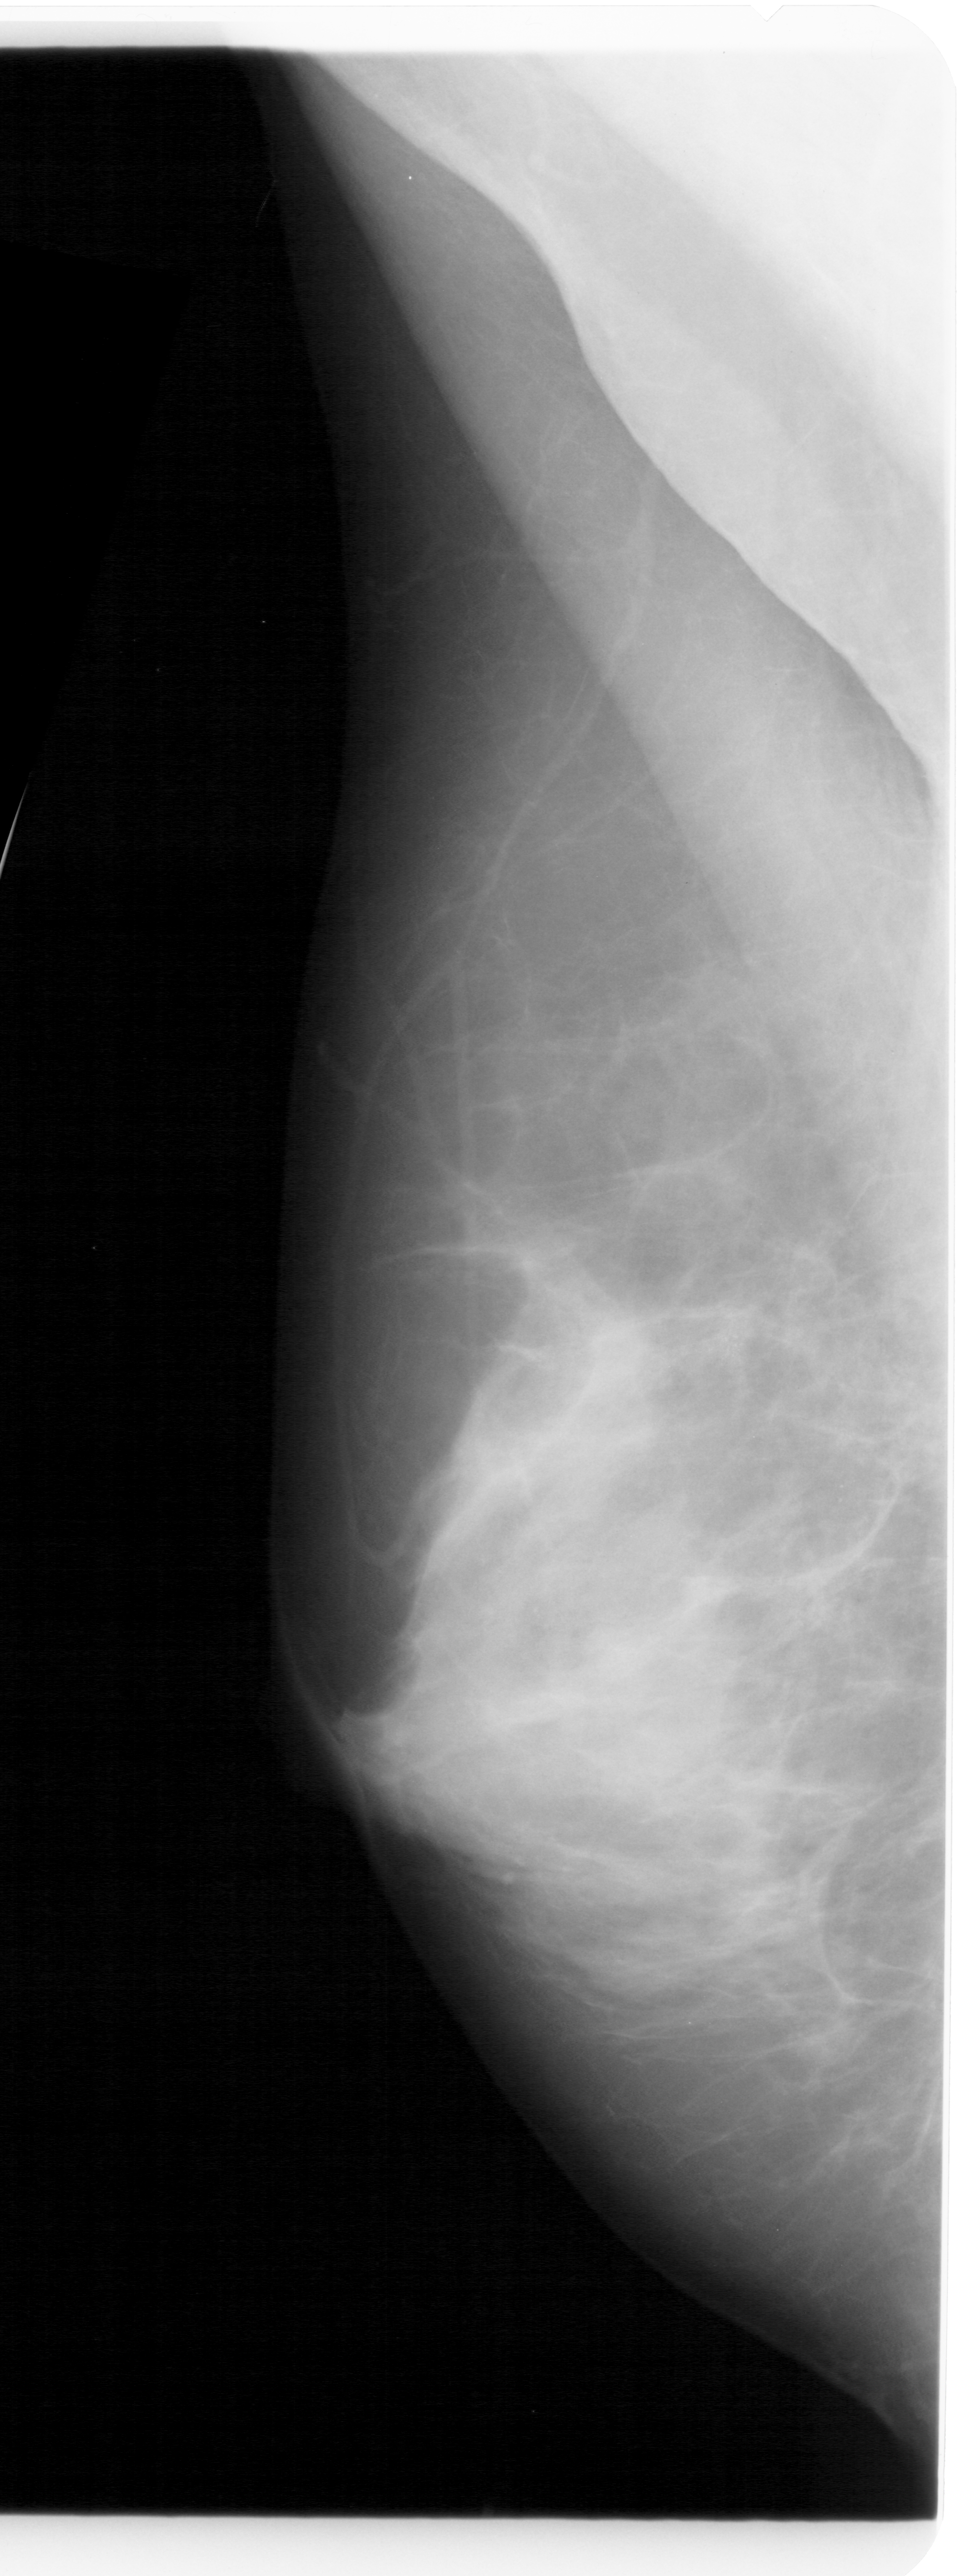
Mammogram (digitized film); left breast; mediolateral oblique (MLO) view; BI-RADS breast density category 4 (scale 1–4); 962 × 2576 image matrix.
Marked abnormalities (boxes around the expert regions of interest):
- calcifications, morphology pleomorphic, distribution clustered; BI-RADS assessment category 4; subtlety rating 1 on a 1 (subtle) to 5 (obvious) scale; pathology (as recorded): malignant: bounding box [x1, y1, x2, y2] px = [696, 1306, 759, 1392]